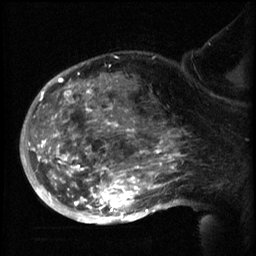
Breast MRI (dynamic contrast-enhanced), one sagittal slice. Position 40 of 60 along the scan axis. 3 images stored at this slice position (order not interpretable as contrast timing). 1.5 T. TE 4.2 ms, TR 8.2 ms. 256 × 256 image matrix, field of view 200 × 200 mm. Female patient, age 50 years.
Annotated regions visible in this slice (semi-automatically segmented with operator editing):
- analysis volume of interest (the breast-tissue region the enhancement analysis was run in; not a lesion): bounding box <50,64,169,217> (left, top, right, bottom; pixels)
- tumour enhancement mask (voxels above the 70 % enhancement threshold inside the analysis volume of interest): <50,70,169,213>